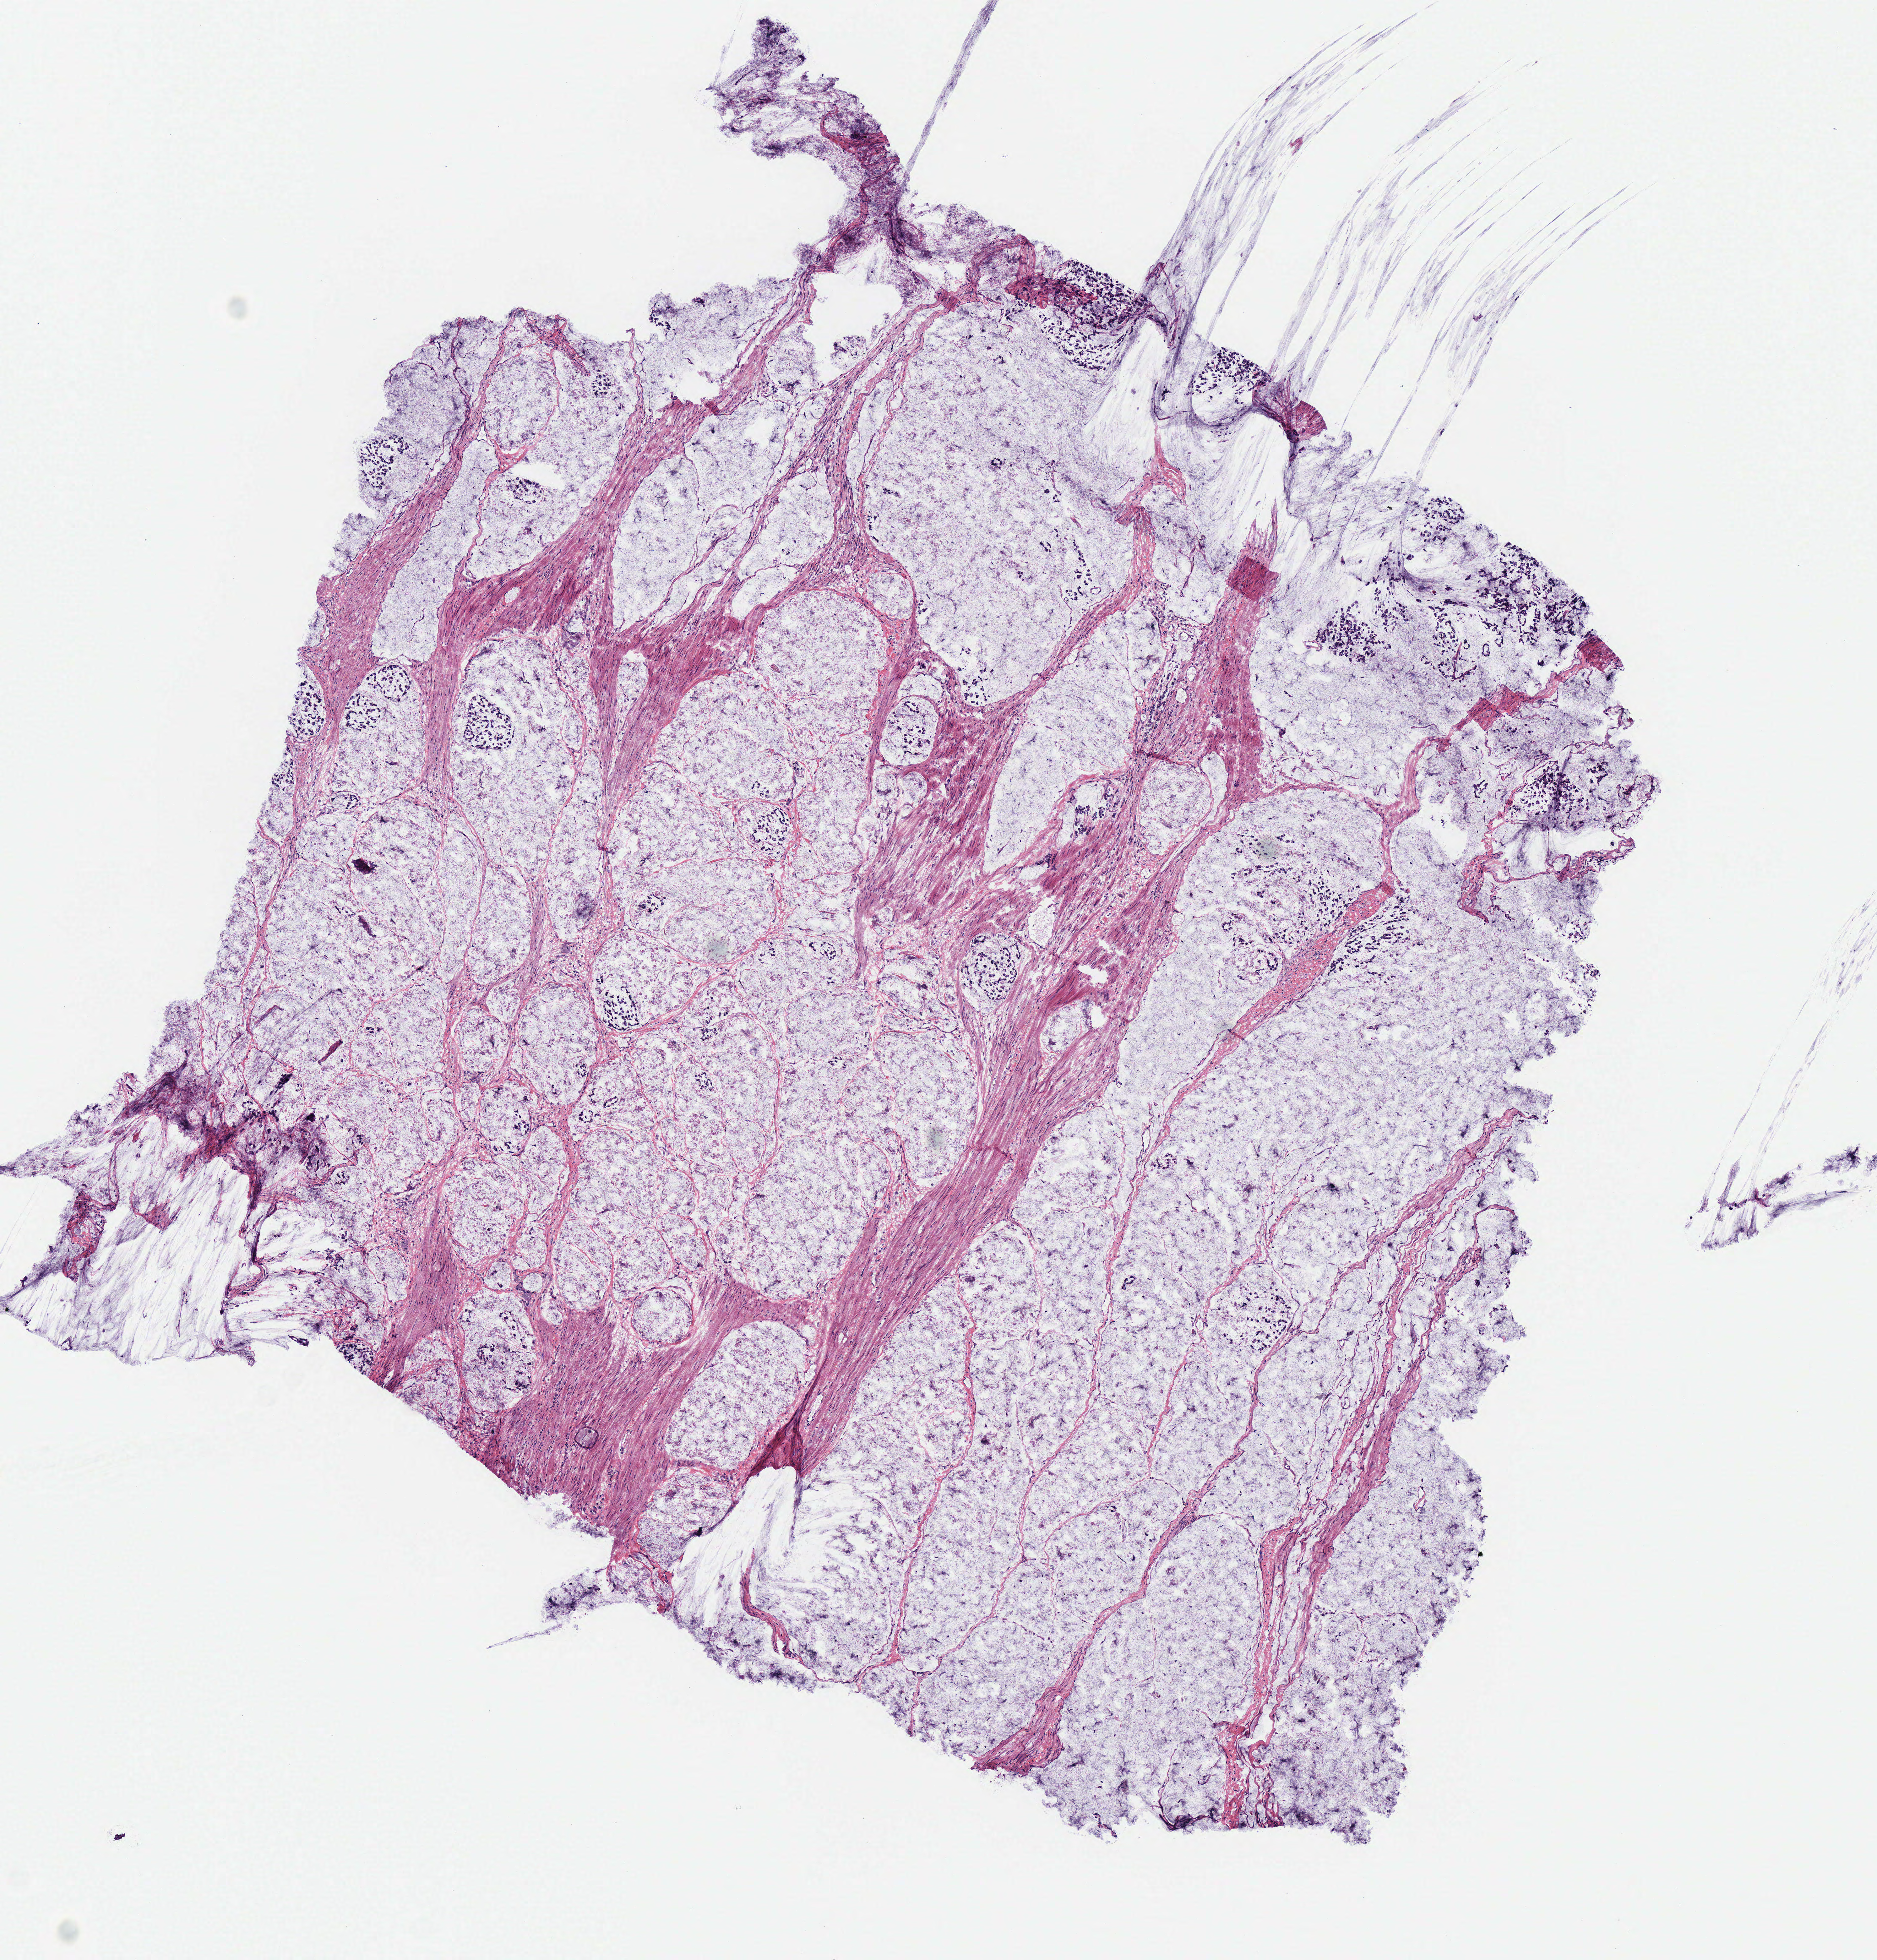
H&E whole-slide image, whole scanned area (about 5.9 x 6.1 mm, from a 40x scan) shown as a low-resolution overview; frozen section from the bottom of the tissue portion; sample: primary tumour, rectum. Female, age 37 years at initial diagnosis. Composition of this section per pathologist review: tumour cells 95%, tumour nuclei 70%, normal cells 0%, stromal cells 5%, necrosis 0%.
• diagnosis: Mucinous adenocarcinoma
• lymph nodes positive (case pathology): 30 of 30 examined